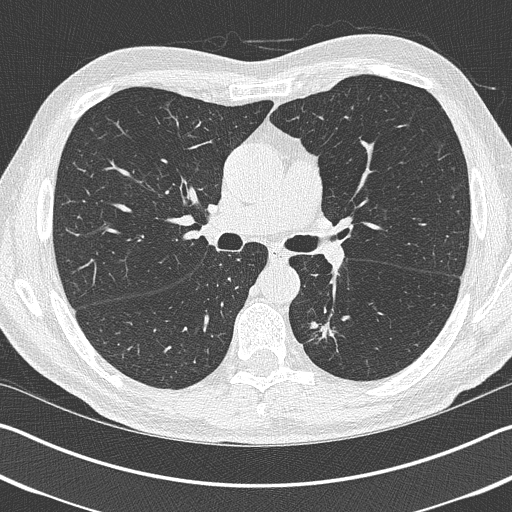
Chest CT (low-dose screening protocol), one axial image, baseline screening round, lung window (W 1500 / L -600 HU), 1 mm slice thickness, 120 kVp, slice 156 of 402 in the series. Male participant, aged 69 years at enrolment. Current smoker at enrolment.
• Expert reader's lesion annotation, bounding box [x1, y1, x2, y2] px = [302, 309, 356, 359].
• Screening reader's record for this exam (one nodule recorded; not confirmed to be the boxed lesion): non-calcified nodule or mass ≥4 mm, left upper lobe, 19 × 19 mm, spiculated (stellate) margins, pre-existing on the prior screen: yes.
• Lung cancer was diagnosed 202 days after this screen: non-small cell carcinoma, left lower lobe, stage IIIA (AJCC 6th edition), 20 mm at pathology.